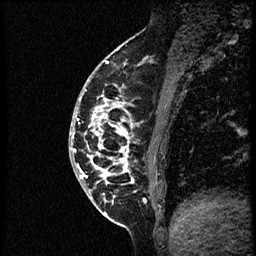
Breast MRI (dynamic contrast-enhanced), one sagittal slice; slice 21 of 56 in the series (ordered by position); dynamic contrast-enhanced study with each time point stored as its own series, time point 2 of 3 at this slice position (early post-contrast, ordered by acquisition time); 1.5 T; TE 4.2 ms, TR 21.3 ms; 2 mm slice thickness; 256 × 256 image matrix, field of view 200 × 200 mm. Female patient, age 41 years. From the clinical record (not read from this slice): setting: breast cancer imaged before/during neoadjuvant chemotherapy; receptor status: HER2-positive.
Annotated regions visible in this slice (semi-automatic segmentation, software-assisted and operator-edited):
- analysis volume of interest (the breast-tissue region the enhancement analysis was run in; not a lesion): bounding box (x1, y1, x2, y2) in pixels: (70, 73, 173, 205)
- tumour enhancement mask (voxels above the 100 % enhancement threshold inside the analysis volume of interest): (72, 80, 134, 183)